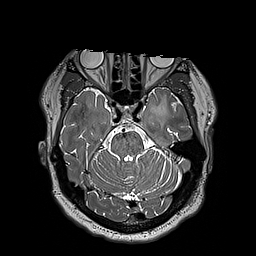
Brain MRI from a brain-tumour surgery series, one axial slice. Position 130 of 192 along the scan axis. 256 × 256 image matrix, field of view 250 × 250 mm. Case-level facts recorded for this patient, not image findings: histopathology: Astrocytoma; WHO grade: 3; IDH mutation: yes.
Structures marked on this image (expert manual segmentation):
- tumour: box from (x=150, y=99) to (x=167, y=118) px